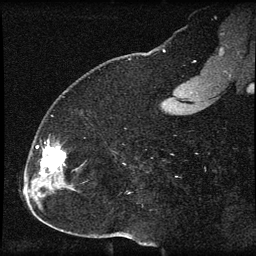
Breast MRI (dynamic contrast-enhanced), one sagittal slice; slice 22 of 60 in the series (ordered by position); dynamic contrast-enhanced series, image 2 of 3 at this slice position (ordered by acquisition); 1.5 T; TE 4.2 ms, TR 8.2 ms; 2 mm slice thickness; 256 × 256 image matrix, field of view 180 × 180 mm. Female patient, age 32 years.
Structures marked on this image (semi-automatically segmented with operator editing):
- analysis volume of interest (the breast-tissue region the enhancement analysis was run in; not a lesion): bounding box [x1, y1, x2, y2] px = [31, 139, 78, 184]
- tumour enhancement mask (voxels above the 70 % enhancement threshold inside the analysis volume of interest): [36, 140, 66, 176]